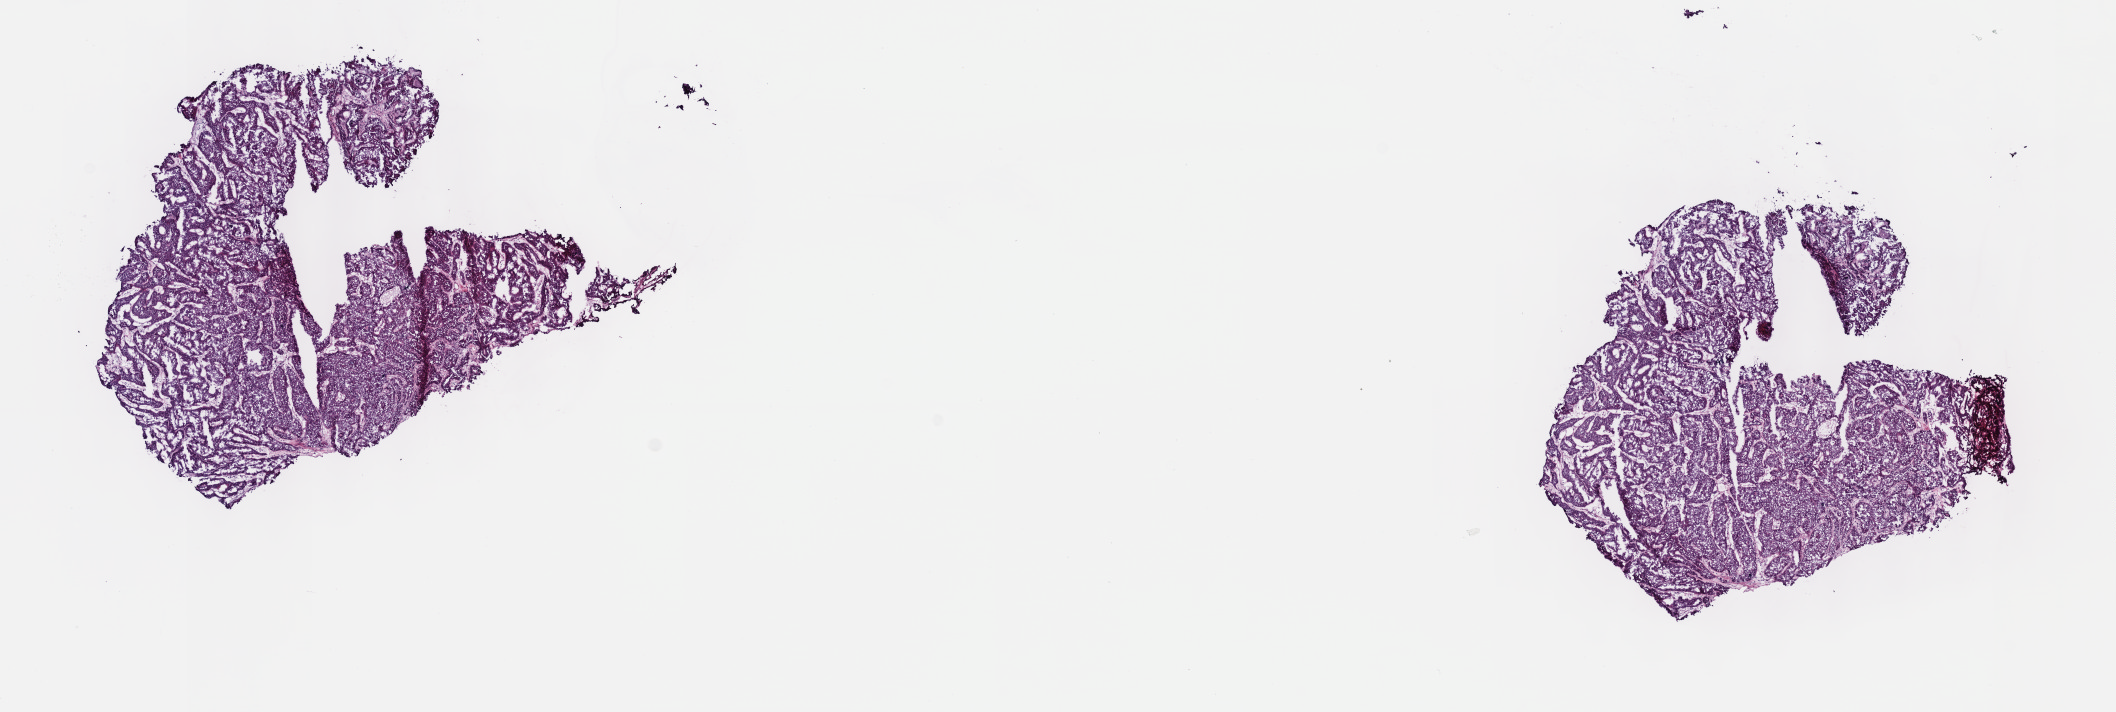
Whole-slide histology image, H&E, whole scanned area (about 17.1 x 5.8 mm, slide scanned at 40x) shown as a low-resolution overview, frozen section from the top of the tissue portion, sample: primary tumour, kidney. Patient: male, age at initial diagnosis 55 years. Pathologist review of this section (percent, as recorded): tumour cells 82%, tumour nuclei 90%, normal cells 0%, stromal cells 15%, necrosis 3%. Infiltration values recorded for this section: lymphocyte infiltration 3%, monocyte infiltration 6%, neutrophil infiltration 1%.
AJCC pathologic stage: I (7th edition). Laterality: right. Diagnosis: Papillary adenocarcinoma, NOS.